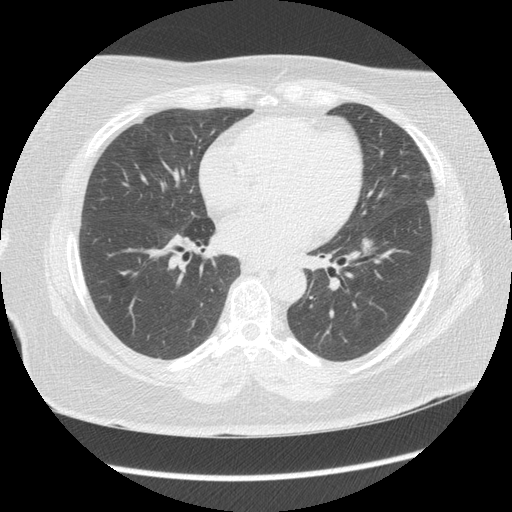
Chest CT (low-dose screening protocol), one axial image, third annual screen, lung window (W 1500 / L -600 HU), standard (soft-tissue) reconstruction kernel (STANDARD), slice 81 of 144 in the series, 512 × 512 image matrix. Female, age 65 years at enrolment. Current smoker at enrolment.
Lesion marked by an expert reader, bounding box (x1, y1, x2, y2) in pixels: (345, 227, 379, 268). The exam's reader record, not a measurement of the box and not confirmed to be the same lesion: non-calcified nodule or mass ≥4 mm, left lower lobe, 130 × 90 mm, poorly defined margins, mixed attenuation, pre-existing on the prior screen: yes; interval growth: yes. Official screen result: positive, other. Lung cancer was diagnosed 35 days after this screen: adenocarcinoma, NOS, left lower lobe, moderately differentiated (G2), stage IA (AJCC 6th edition), 12 mm at pathology.